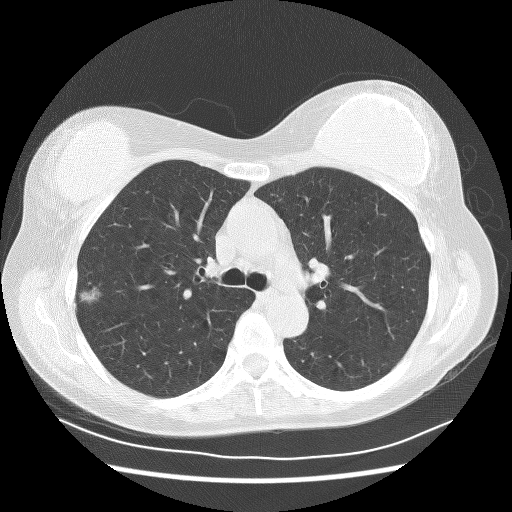
Axial slice from a low-dose chest CT screening exam; first (baseline) screen; lung window (W 1500 / L -600 HU); 2.5 mm slice thickness; lung (sharp) reconstruction kernel (BONE). Female participant, aged 58 years at enrolment. Former smoker at enrolment.
Expert-annotated lung lesion, bounding box <65,272,114,312> (left, top, right, bottom; pixels). The screening reader recorded 2 non-calcified nodules or masses ≥4 mm on this exam; which of them this box marks is not recorded. Lung cancer was diagnosed 510 days after this screen: bronchiolo-alveolar adenocarcinoma, NOS, right upper lobe, well differentiated (G1), stage IA (AJCC 6th edition).